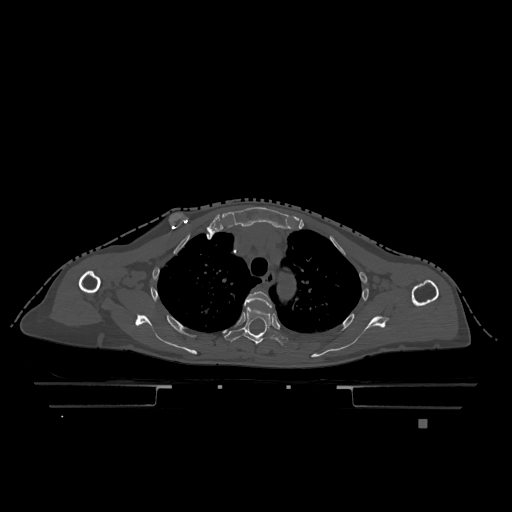
CT including the spine, one axial slice; position 891 of 1317 along the scan axis; bone window (W 1800 / L 400 HU); 0.5 mm slice thickness; 512 × 512 image matrix. Female patient, age 74 years. Case-level facts recorded for this patient, not image findings: primary cancer: lung; vertebrae with lytic lesions (as recorded): T1, T4, T5, T6, L4, L5.
Outlined on this slice (semi-automatic segmentation, software-assisted and operator-edited):
- T3 vertebra: bounding box (x1, y1, x2, y2) in pixels: (245, 291, 272, 307)
- T4 vertebra: (224, 306, 288, 346)